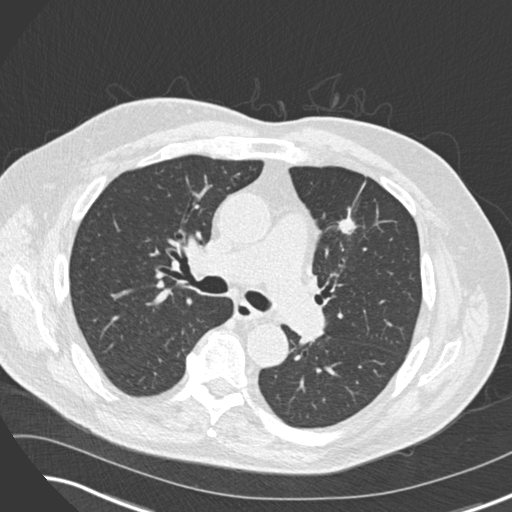
Axial slice from a low-dose chest CT screening exam, third annual screen, lung window (W 1500 / L -600 HU), 2 mm slice thickness, standard (soft-tissue) reconstruction kernel (B30f). Male, age 74 years at enrolment.
Expert-annotated lung lesion, bounding box (x1, y1, x2, y2) in pixels: (320, 198, 377, 248). Reader record for this screening exam (exam-level; its link to the box is not recorded): non-calcified nodule or mass ≥4 mm, left upper lobe, 12 × 10 mm, spiculated (stellate) margins, soft tissue attenuation, pre-existing on the prior screen: yes; interval growth: yes. Participant outcome: lung cancer diagnosed 349 days after this screen — adenocarcinoma, NOS, left upper lobe, poorly differentiated (G3), stage IIIA (AJCC 6th edition), 27 mm at pathology.